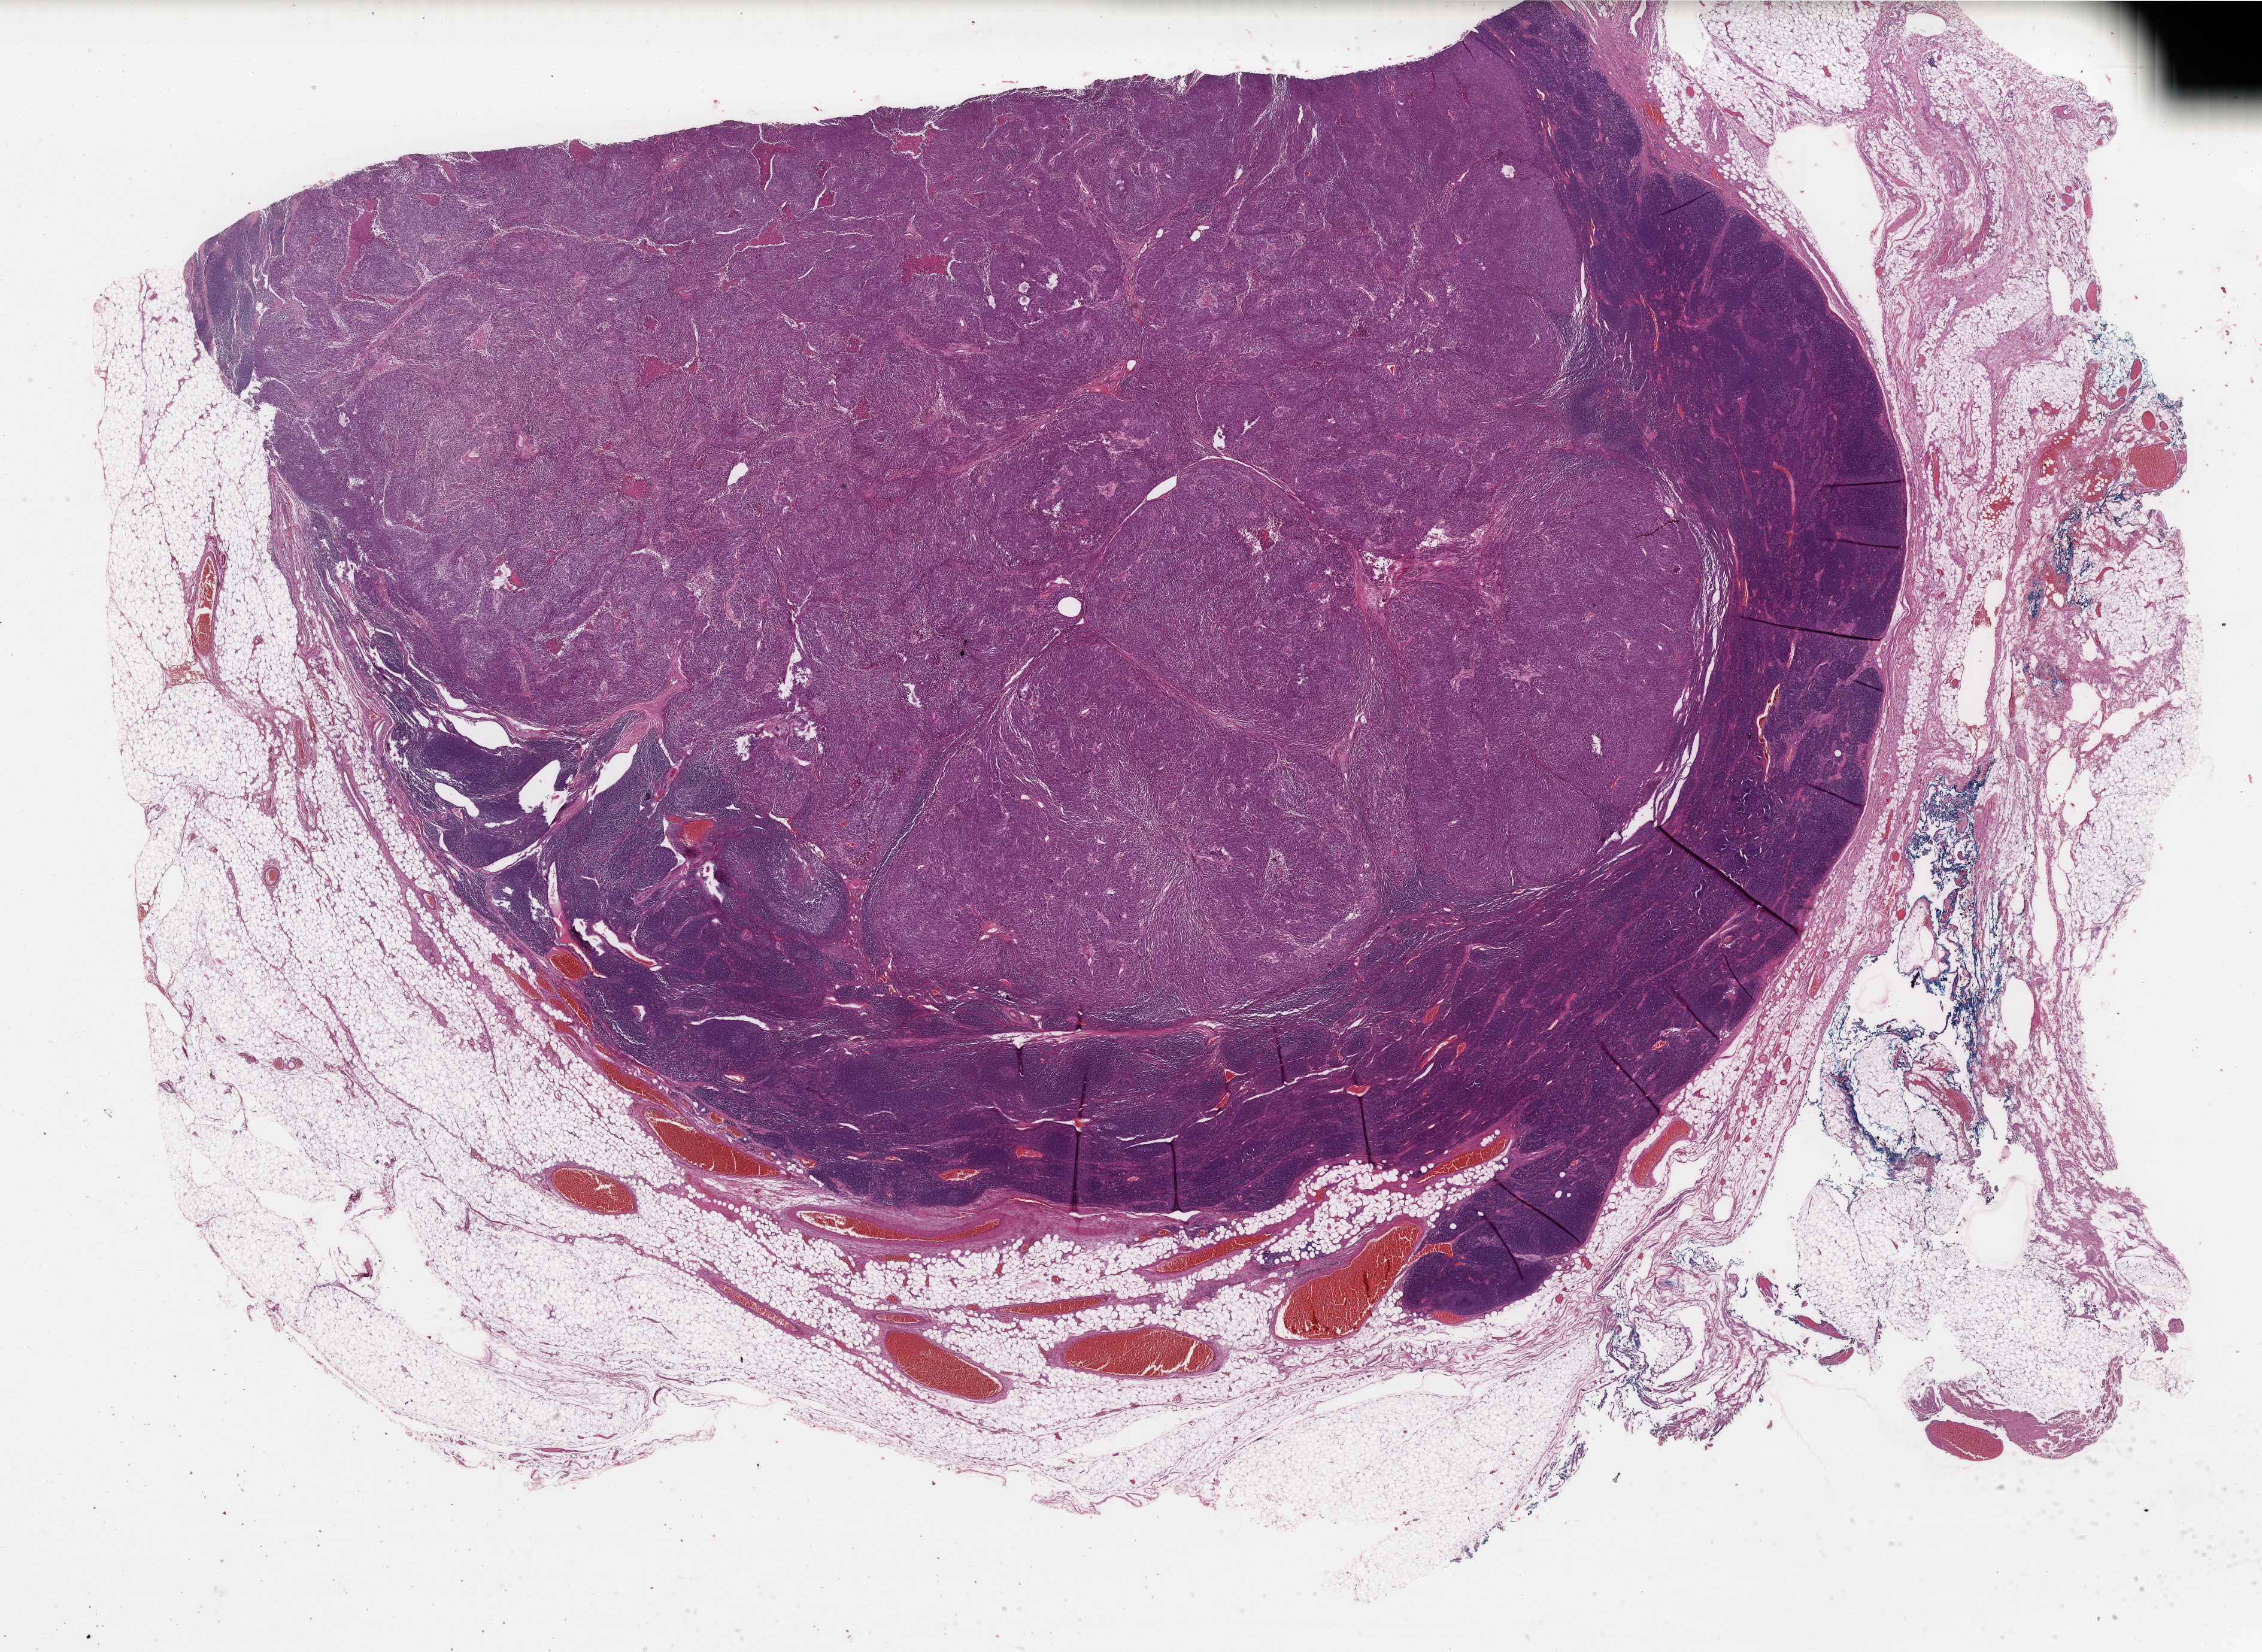
Whole-slide histology image, H&E-stained, whole scanned area (about 30.0 x 21.9 mm, from a 40x scan) shown as a low-resolution overview, formalin-fixed paraffin-embedded (FFPE) diagnostic section, primary tumour sample from the skin. Male patient; age at initial diagnosis 39 years.
Histologic diagnosis: Malignant melanoma, NOS.